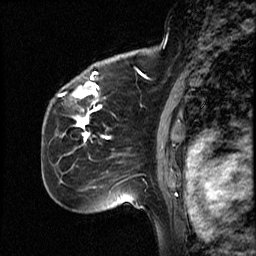
Breast MRI (dynamic contrast-enhanced), one sagittal slice; slice 36 of 50 in the series (ordered by position); dynamic contrast-enhanced study with each time point stored as its own series, time point 2 of 4 at this slice position (early post-contrast, ordered by acquisition time); 1.5 T; TE 4.2 ms, TR 18.5 ms; 256 × 256 image matrix, field of view 200 × 200 mm. Female patient, age 44 years. From the clinical record (not read from this slice): setting: breast cancer imaged before/during neoadjuvant chemotherapy; receptor status: HR-positive, HER2-negative.
Annotated regions visible in this slice (semi-automatic segmentation, software-assisted and operator-edited):
- analysis volume of interest (the breast-tissue region the enhancement analysis was run in; not a lesion): bounding box (x1, y1, x2, y2) in pixels: (59, 80, 114, 206)
- tumour enhancement mask (voxels above the 100 % enhancement threshold inside the analysis volume of interest): (59, 95, 103, 142)